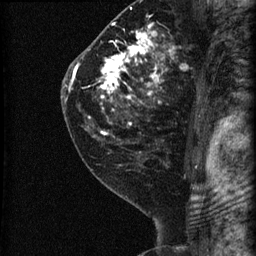
Breast MRI (dynamic contrast-enhanced), one sagittal slice. Position 44 of 60 along the scan axis. Dynamic contrast-enhanced series, image 2 of 3 at this slice position (ordered by acquisition). 1.5 T. TE 4.2 ms, TR 22.7 ms. 1.8 mm slice thickness. 256 × 256 image matrix. Patient: female, 45 years. From the clinical record (not read from this slice): setting: breast cancer imaged before/during neoadjuvant chemotherapy; receptor status: HR-positive, HER2-negative.
Structures marked on this image (semi-automatically segmented with operator editing):
- analysis volume of interest (the breast-tissue region the enhancement analysis was run in; not a lesion): bounding box <74,11,205,140> (left, top, right, bottom; pixels)
- tumour enhancement mask (voxels above the 90 % enhancement threshold inside the analysis volume of interest): <74,23,172,135>